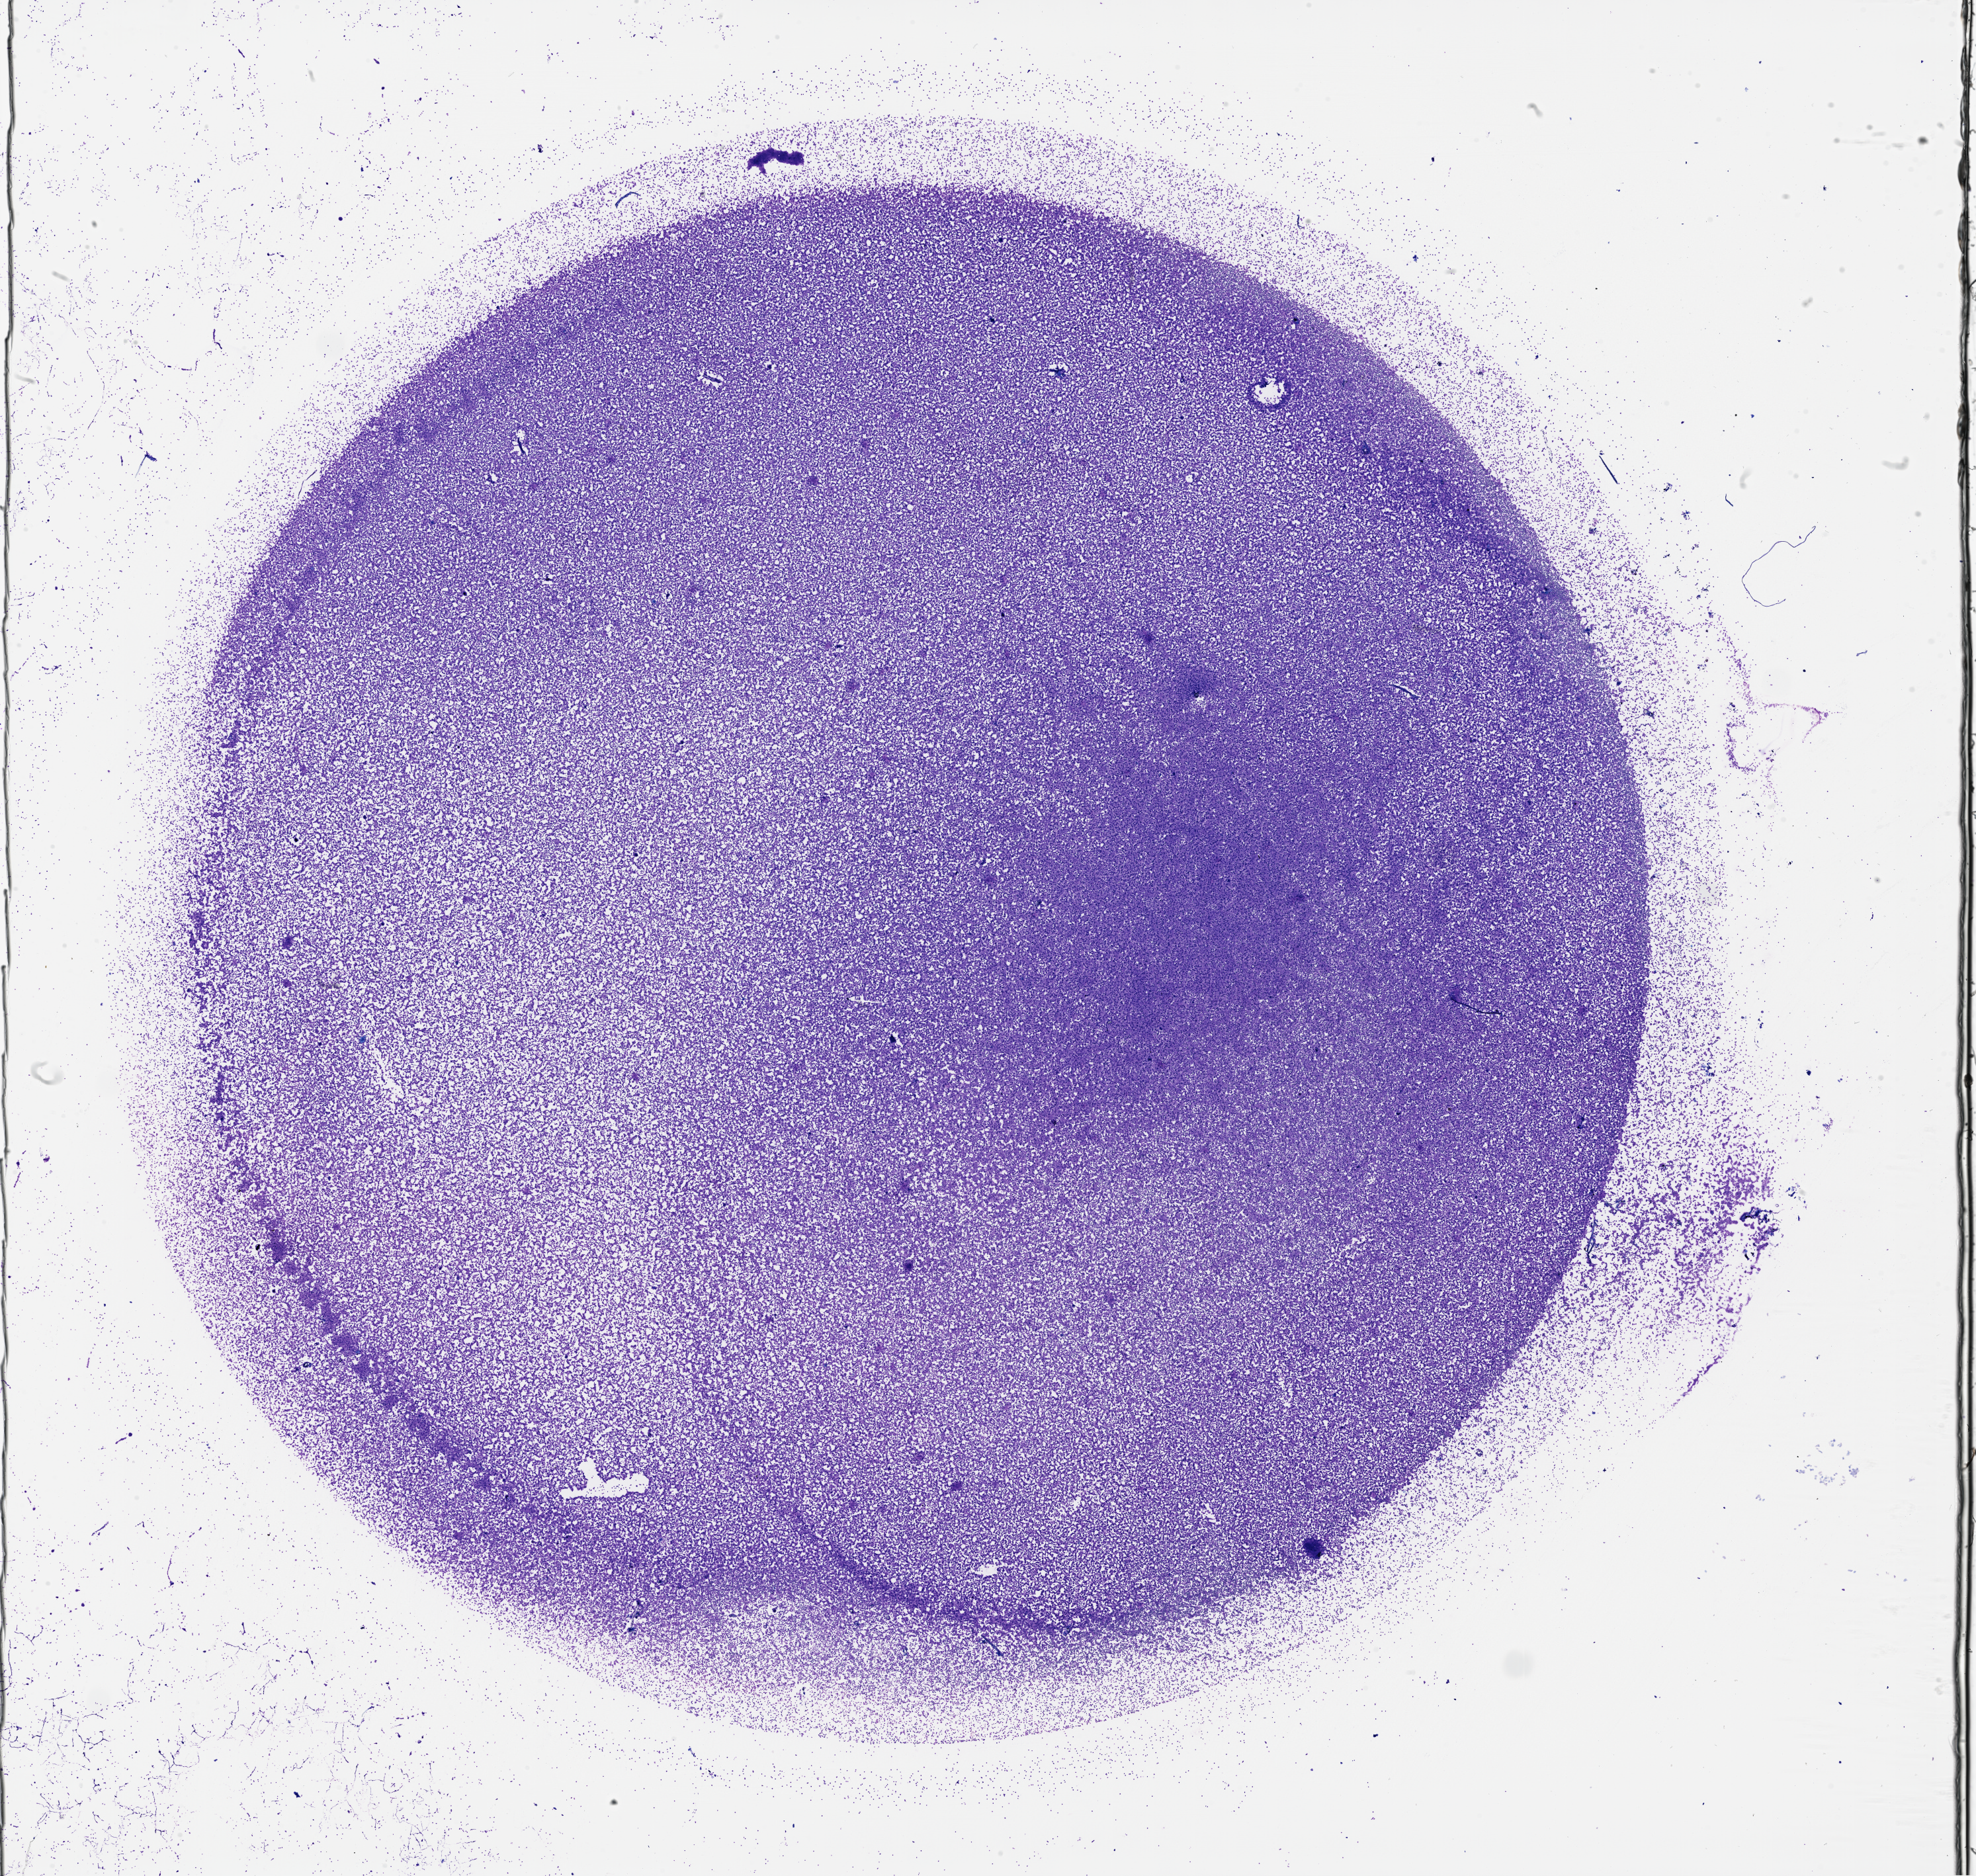
Digitized Hematoxylin and eosin (H&E) stained tissue section (whole slide), a low-resolution overview of the entire scanned area, about 24.1 x 22.9 mm (from a 40x scan). Bone marrow (leukaemic) sample. Female, 72 y/o.
Diagnosis: Acute Myeloid Leukemia.